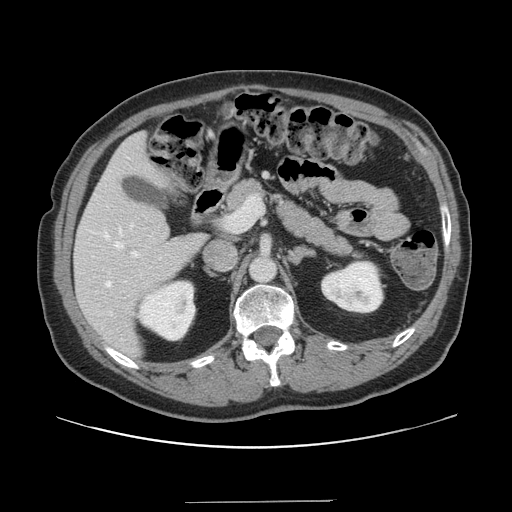
Contrast-enhanced abdominal CT, one axial slice. Slice 80 of 151 in the series (ordered by position). 120 kVp. Intravenous contrast given. Soft-tissue window (W 400 / L 40 HU). 2.5 mm slice thickness. 512 × 512 image matrix, field of view 399 × 399 mm. Male patient, age 63 years. From the clinical record (not read from this slice): diagnosis: colorectal cancer liver metastases, imaged before liver resection; multiple liver metastases: no; largest metastasis: 2.1 cm; disease in both lobes: no.
Annotated regions visible in this slice (manually delineated by an expert):
- hepatic veins: box from (x=105, y=229) to (x=123, y=287) px
- liver: (x=75, y=133)–(x=206, y=357)
- planned liver remnant (the part of the liver to remain after resection): (x=75, y=133)–(x=206, y=357)
- portal vein (with intrahepatic branches): (x=131, y=196)–(x=262, y=258)